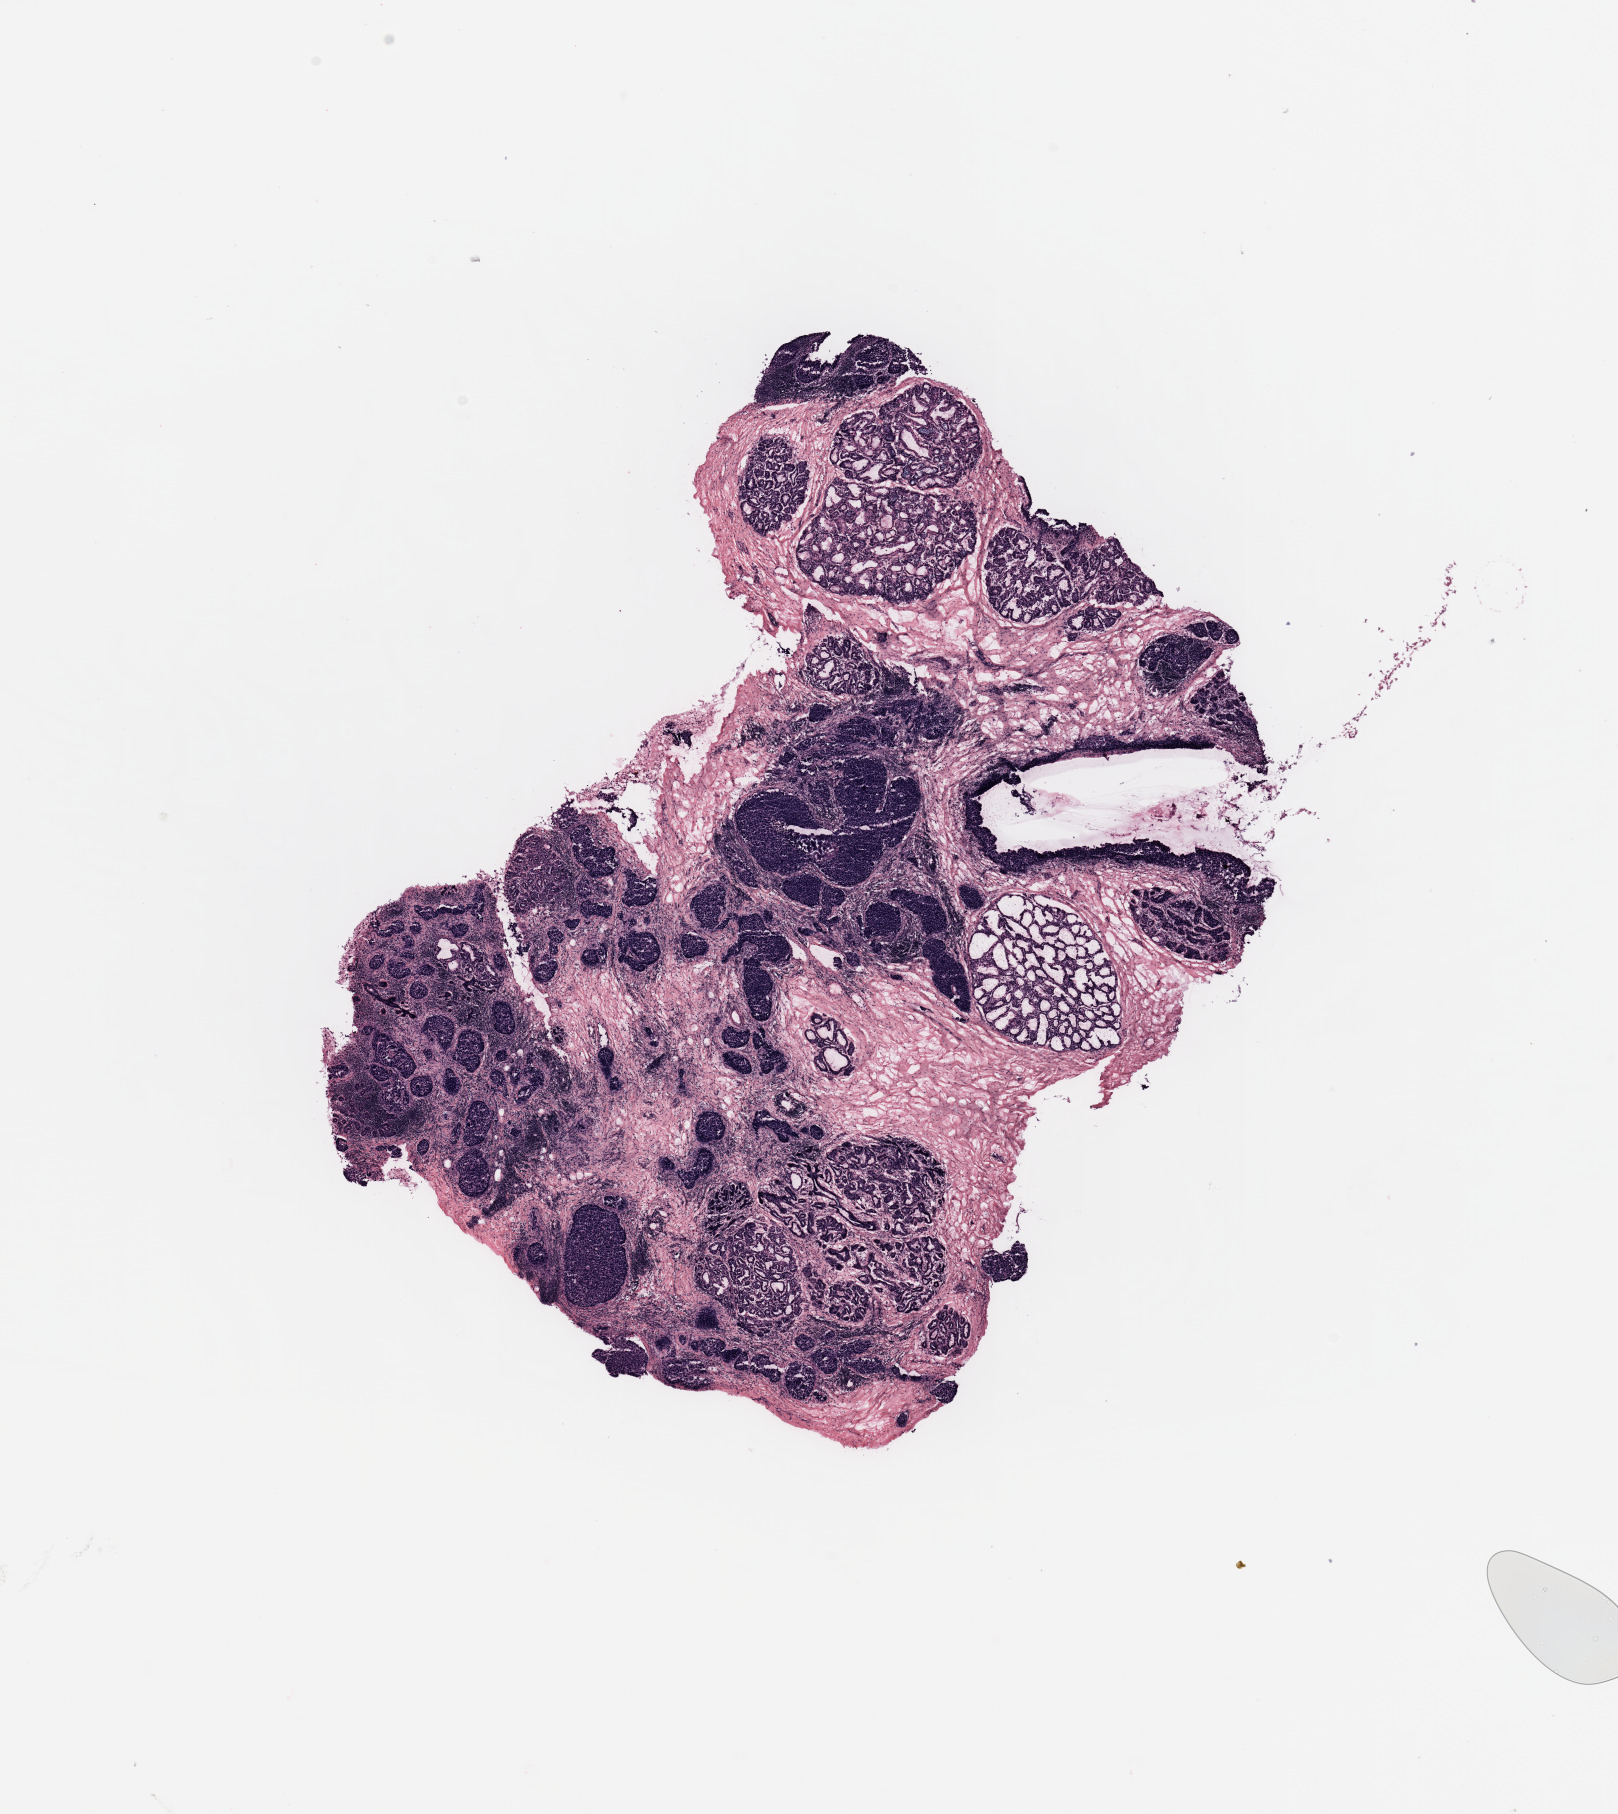
Hematoxylin and eosin (H&E) stained whole-slide image, shown as a low-resolution overview of the whole scanned area (about 12.8 x 14.3 mm). Breast, tumour tissue. Patient: female, age 40 years.
* histologic diagnosis: Infiltrating duct carcinoma, NOS
* AJCC pathologic stage: IIB